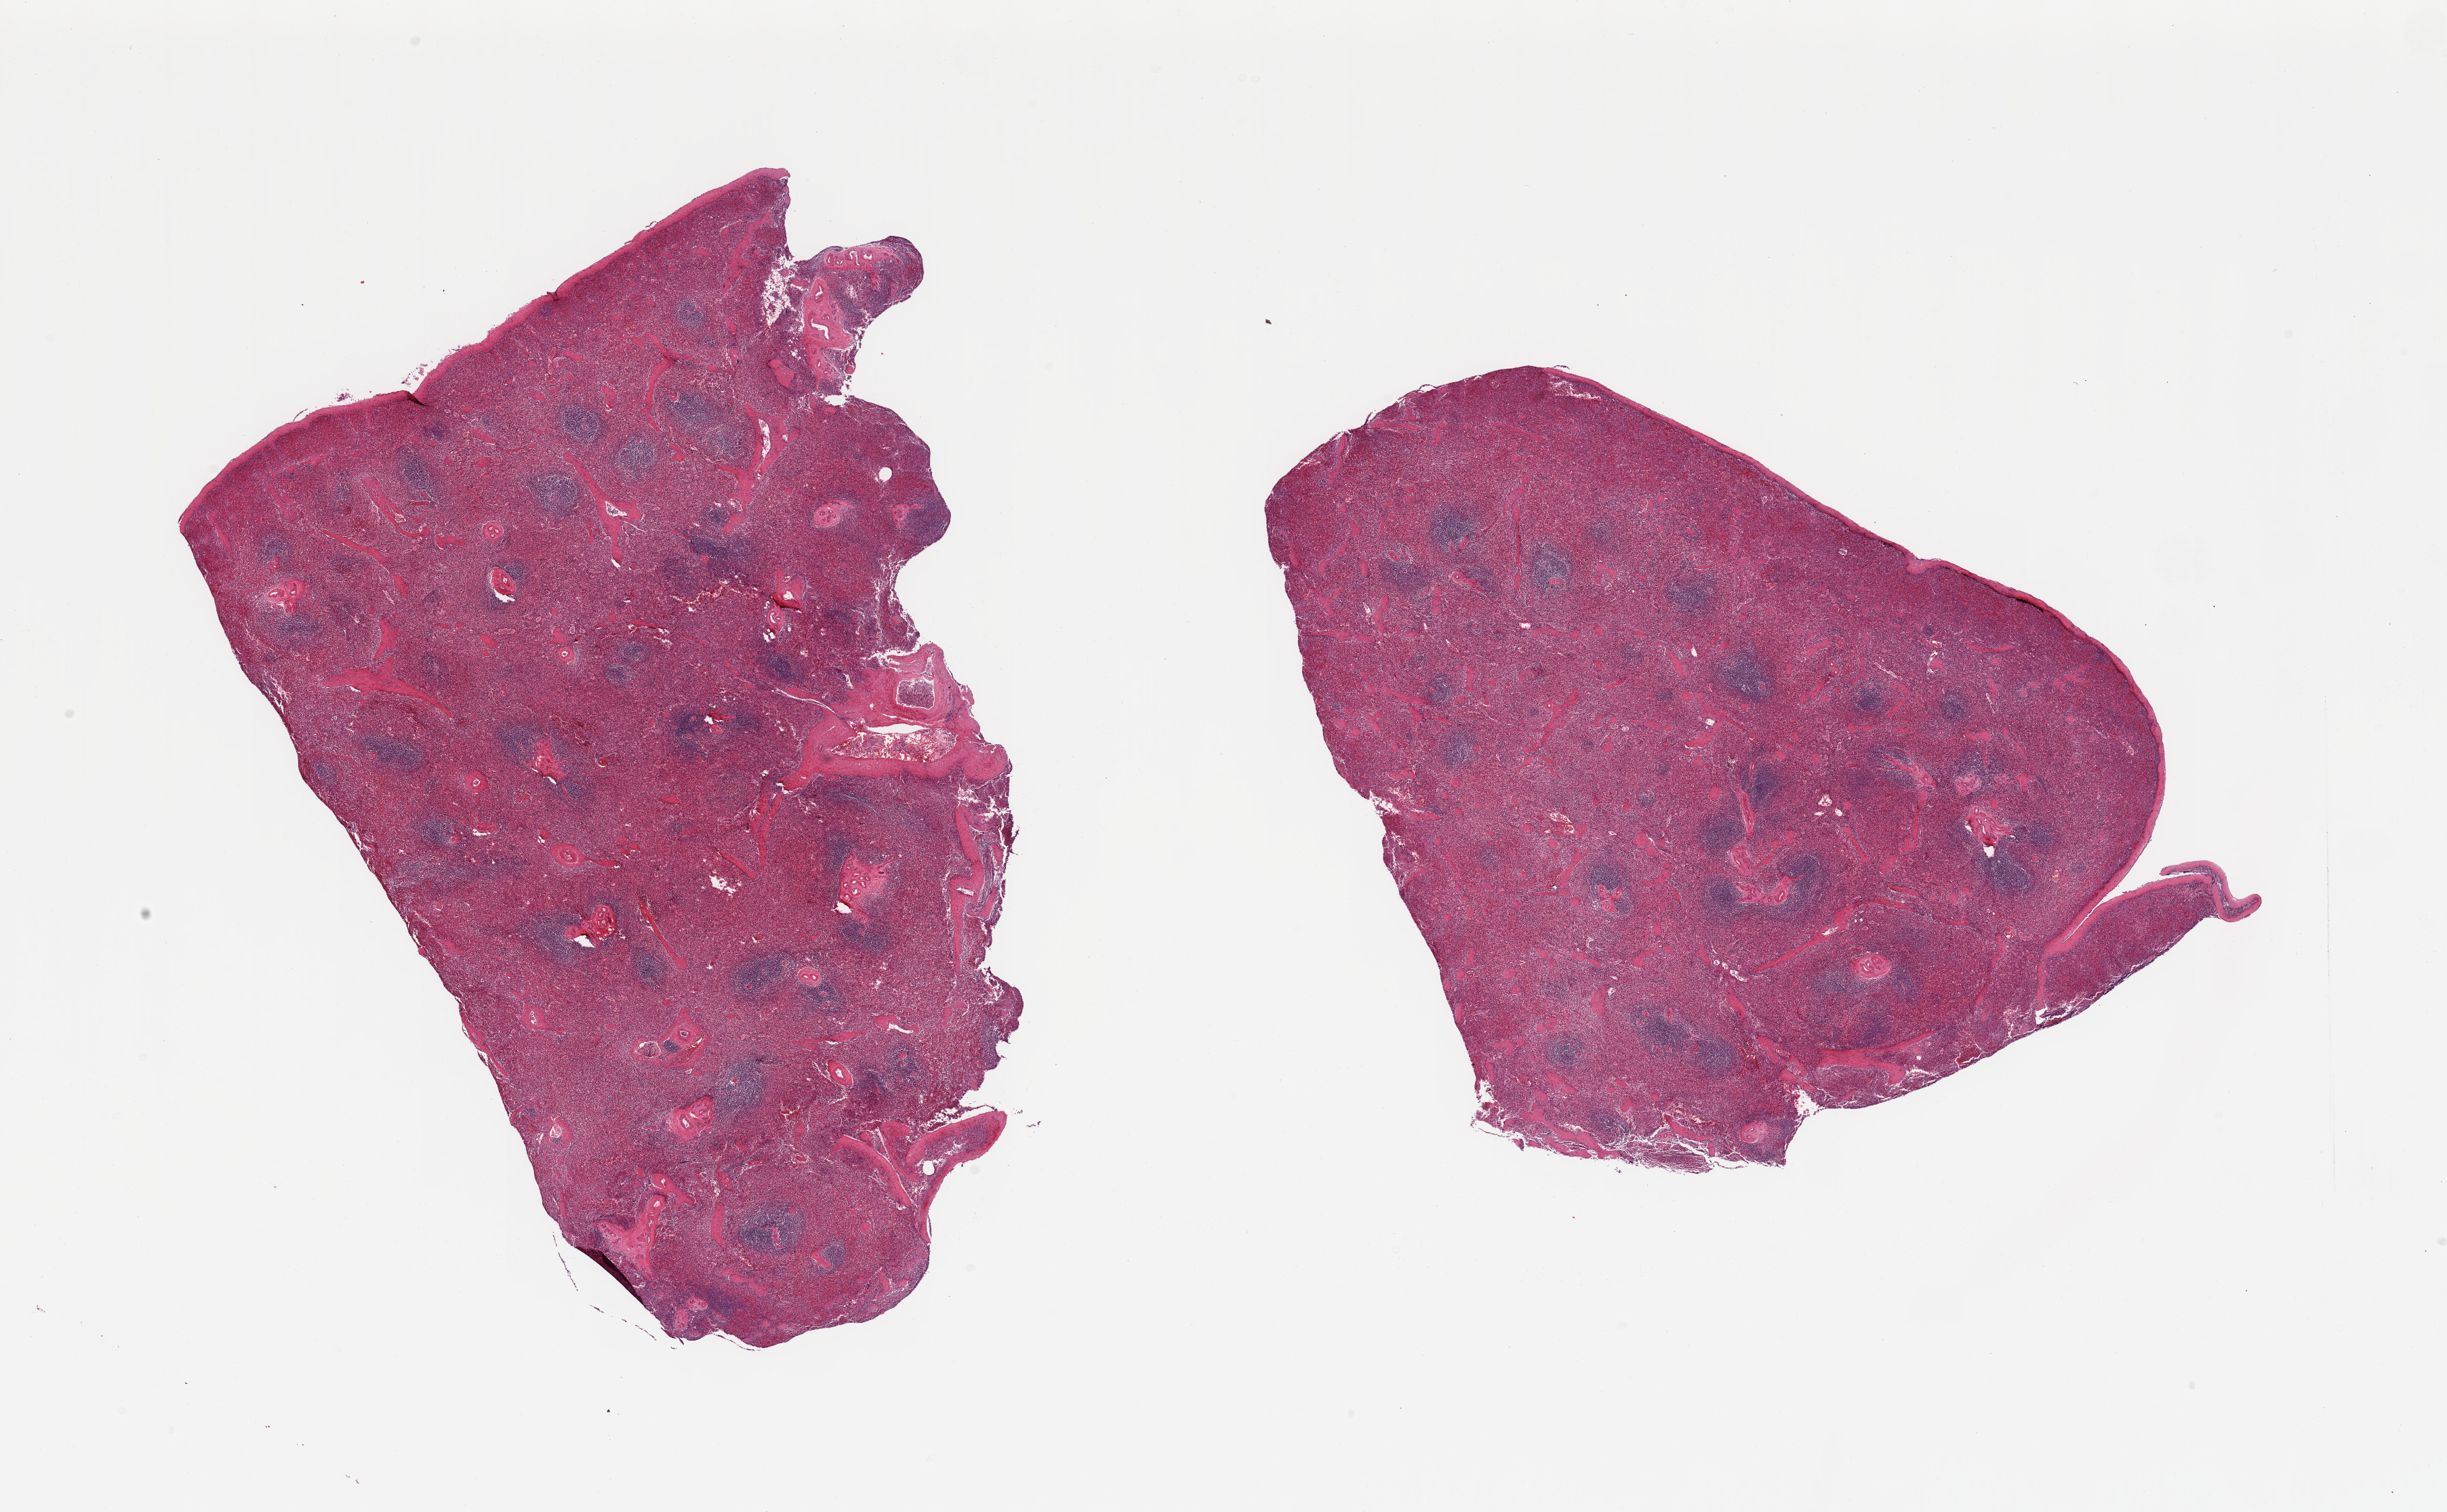
Whole-slide image, H&E stain, low-resolution overview of the scanned area, about 28.5 x 17.6 mm, PAXgene-fixed, paraffin-embedded tissue, sampled site (target tissue): spleen, donor tissue sample. Donor sex: male.
Pathologist's review note for this sample: 2 pieces; congestion; capsule included.